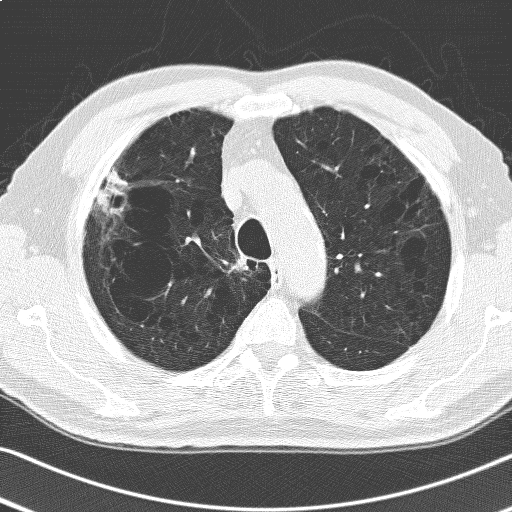
Low-dose screening chest CT, one axial slice. Position 132 of 168 along the scan axis. 120 kVp. Lung window (W 1500 / L -600 HU). 512 × 512 image matrix, field of view 336 × 336 mm.
Annotated regions visible in this slice (outlined manually by an expert reader):
- lesion 1 (tumor, upper lobe of right lung): bounding box [x1, y1, x2, y2] px = [97, 169, 129, 215]